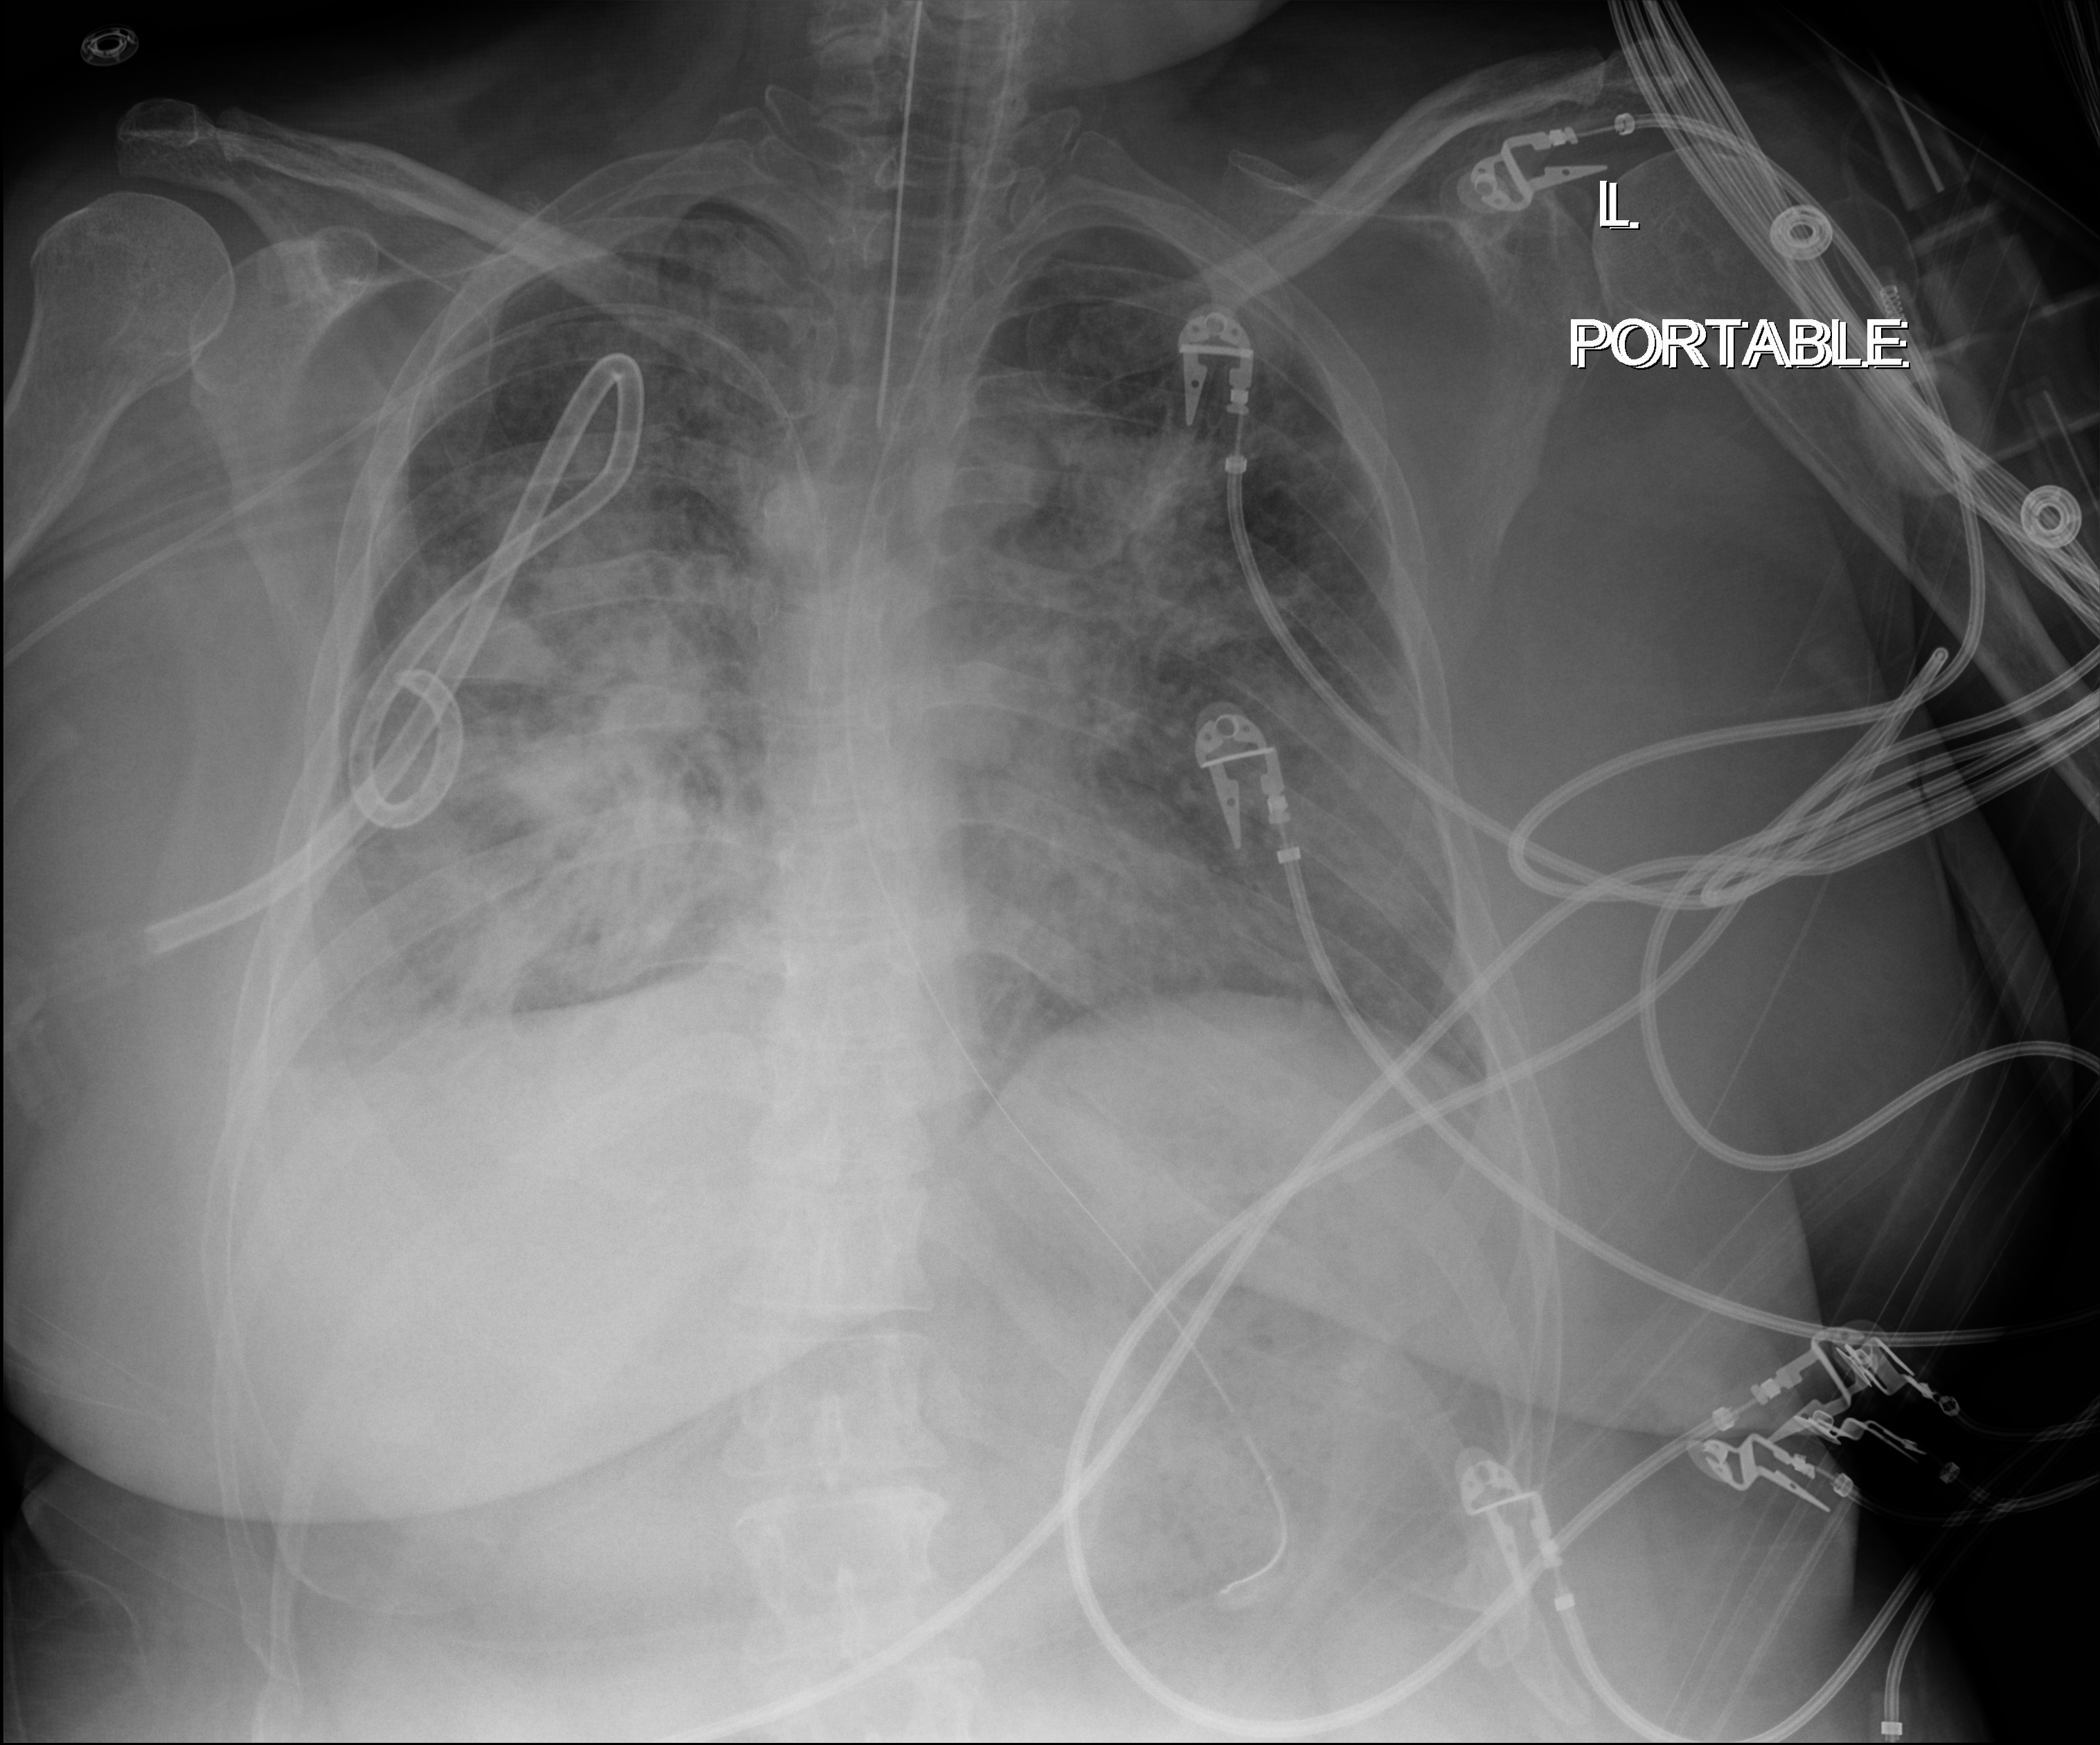
Chest X-ray (portable), anteroposterior (AP) projection. Patient hospitalised with COVID-19, aged 18–59 years.
Hospital-stay facts (about this admission, not read from this image; timing relative to this image not recorded): mechanically ventilated during this hospital stay: yes; admitted to intensive care during this hospital stay: yes.